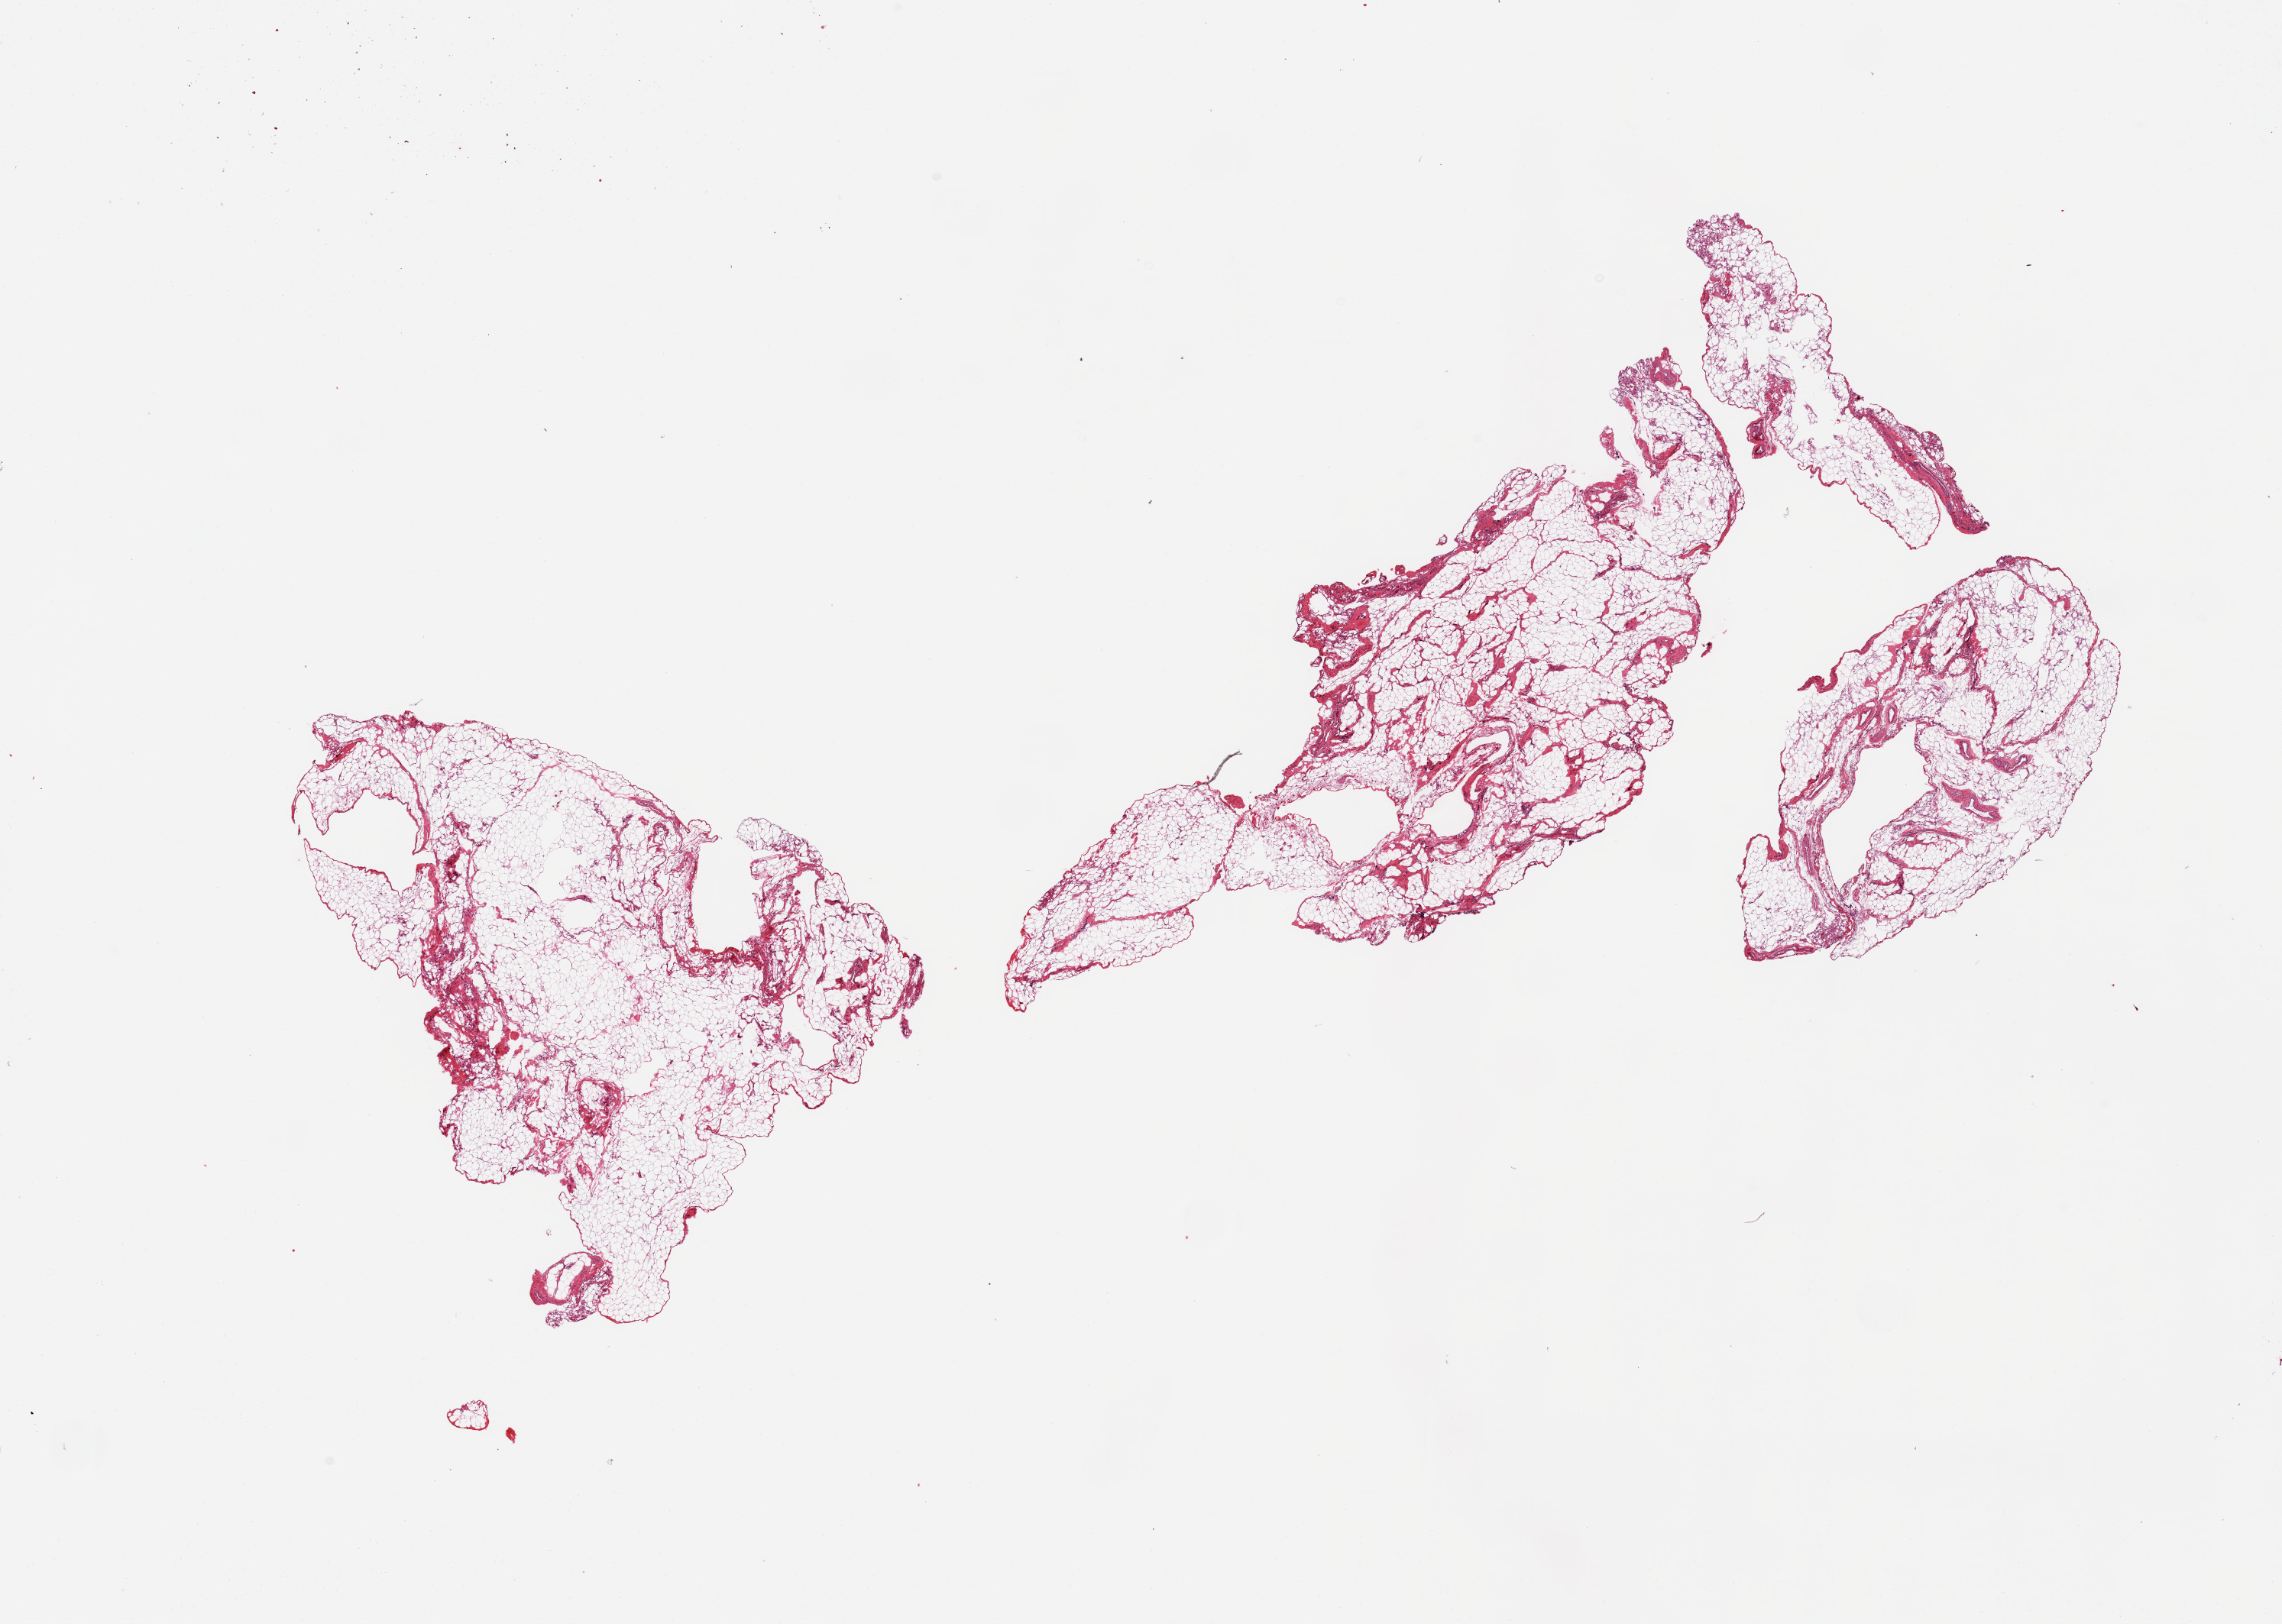
Digitized haematoxylin and eosin-stained section, brightfield — low-resolution overview of the scanned area, about 23.6 x 16.8 mm; PAXgene-fixed paraffin-embedded (PFPE) section; section of omentum (target tissue); donor tissue sample.
* reviewer comment on this tissue sample: 4 pieces; 5% fibrous content